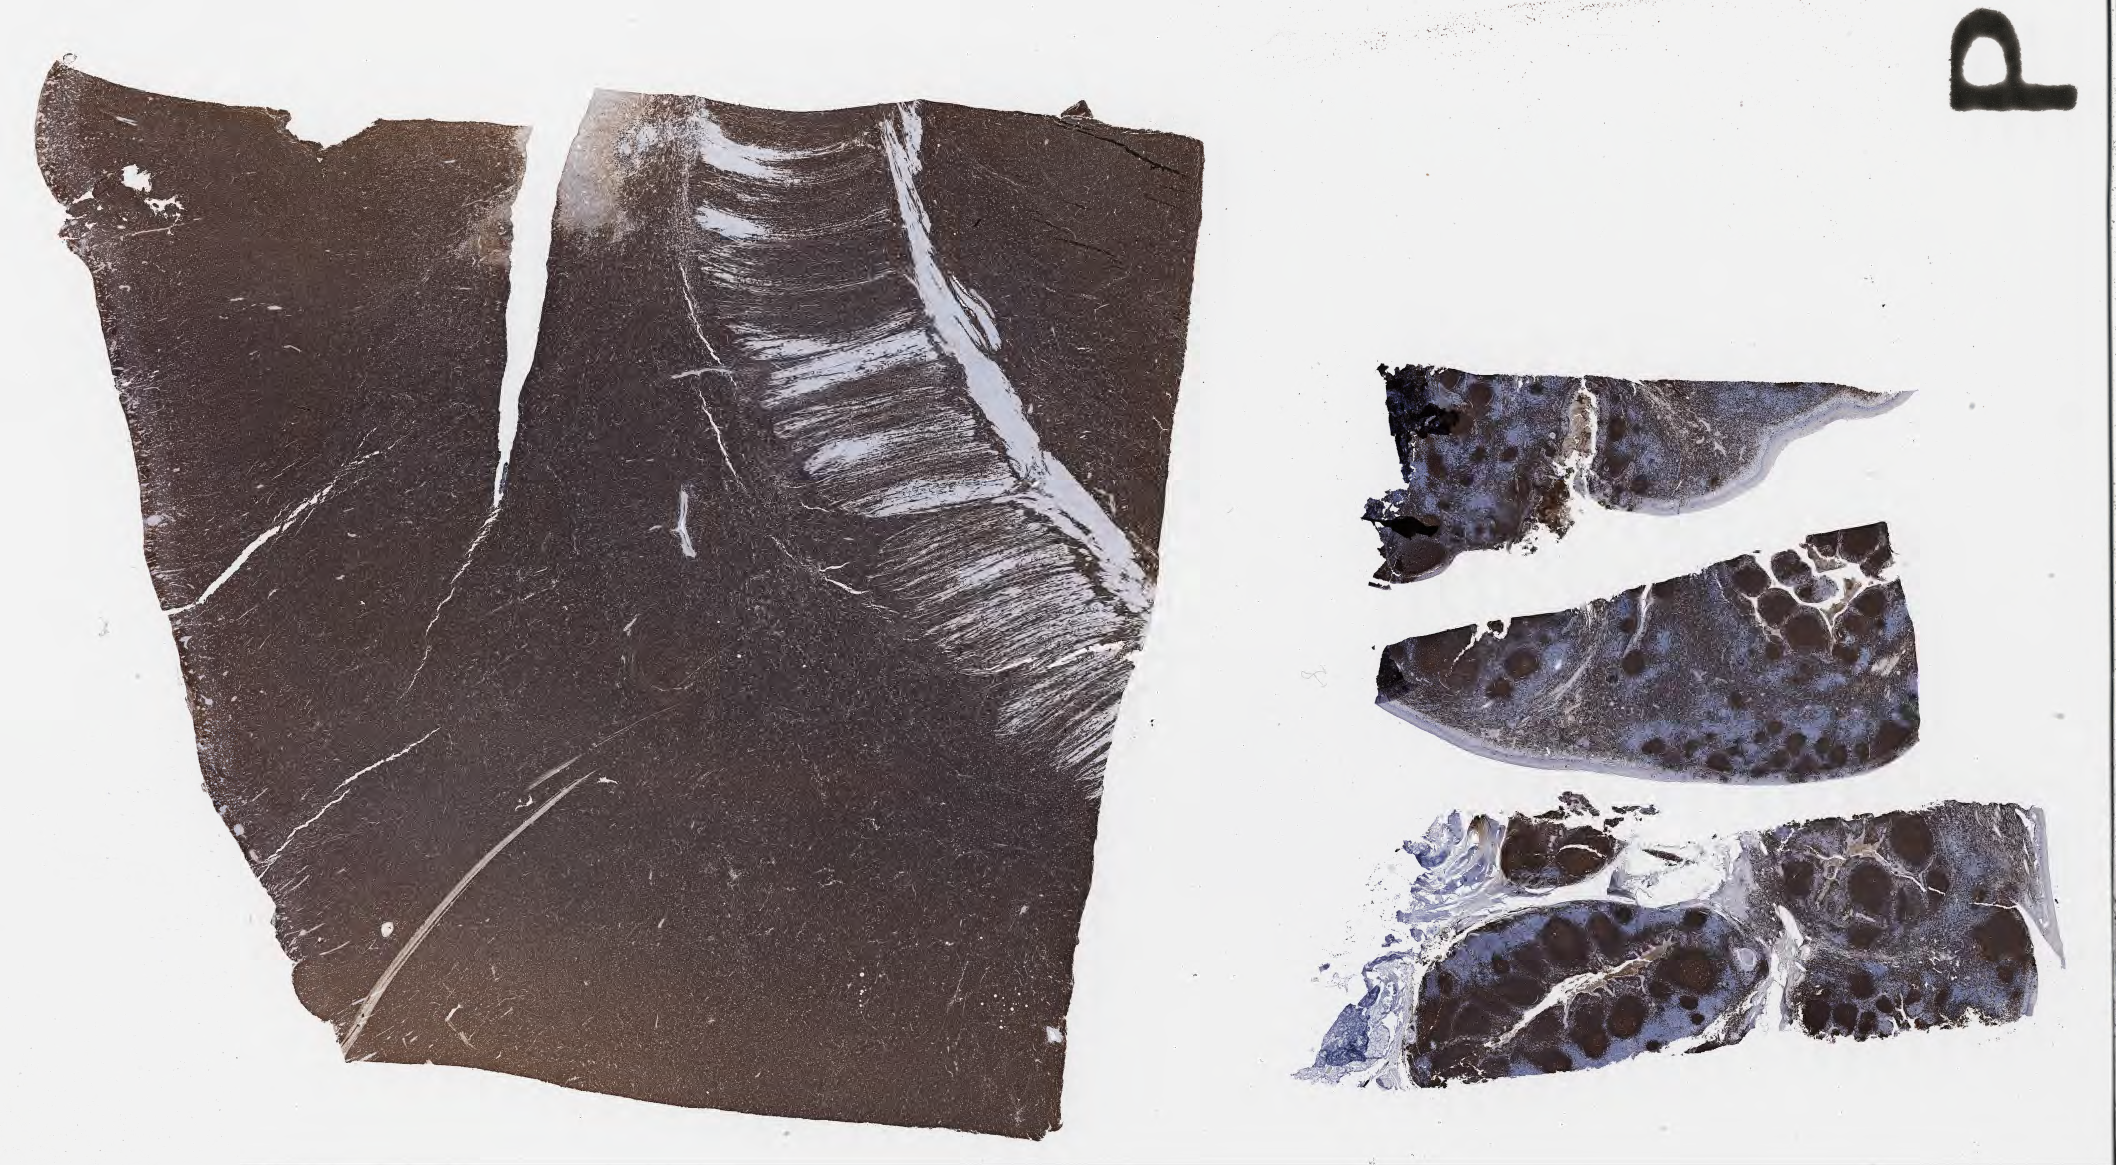
Immunohistochemistry (IHC) whole-slide image stained for CD20 — low-resolution overview of the scanned area, about 34.2 x 18.8 mm. Tumor tissue. Anatomic site: colon. Patient: male, aged 14.
Histologic diagnosis: Burkitt lymphoma, NOS.